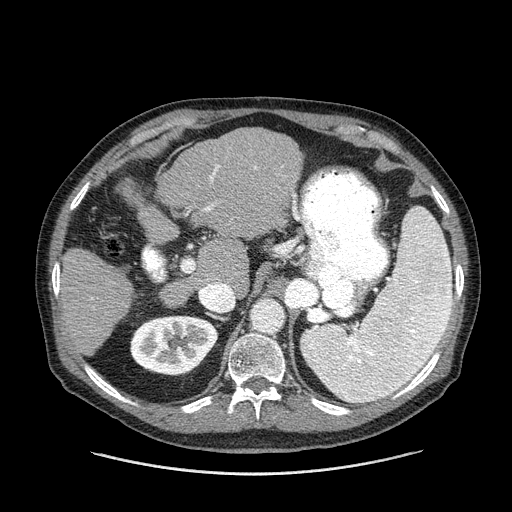
Contrast-enhanced abdominal CT (liver protocol), one axial slice. Position 86 of 180 along the scan axis. Reconstruction kernel STANDARD. One of 2 acquisitions stored at this slice position. Soft-tissue window (W 400 / L 40 HU). 2.5 mm slice thickness. 512 × 512 image matrix. From the clinical record (not read from this slice): diagnosis: hepatocellular carcinoma (patient treated with transarterial chemoembolisation; whether this scan precedes or follows treatment is not stated here); TNM stage (as recorded): Stage-II; Child-Pugh class: A; tumour size: 2.8 cm.
Outlined on this slice (semi-automatically segmented with operator editing):
- liver parenchyma outside the tumour (the mass and vessels are separate outlines, so this box may not span the whole liver): box from (x=58, y=128) to (x=302, y=356) px
- liver vessels: (x=58, y=165)–(x=258, y=300)